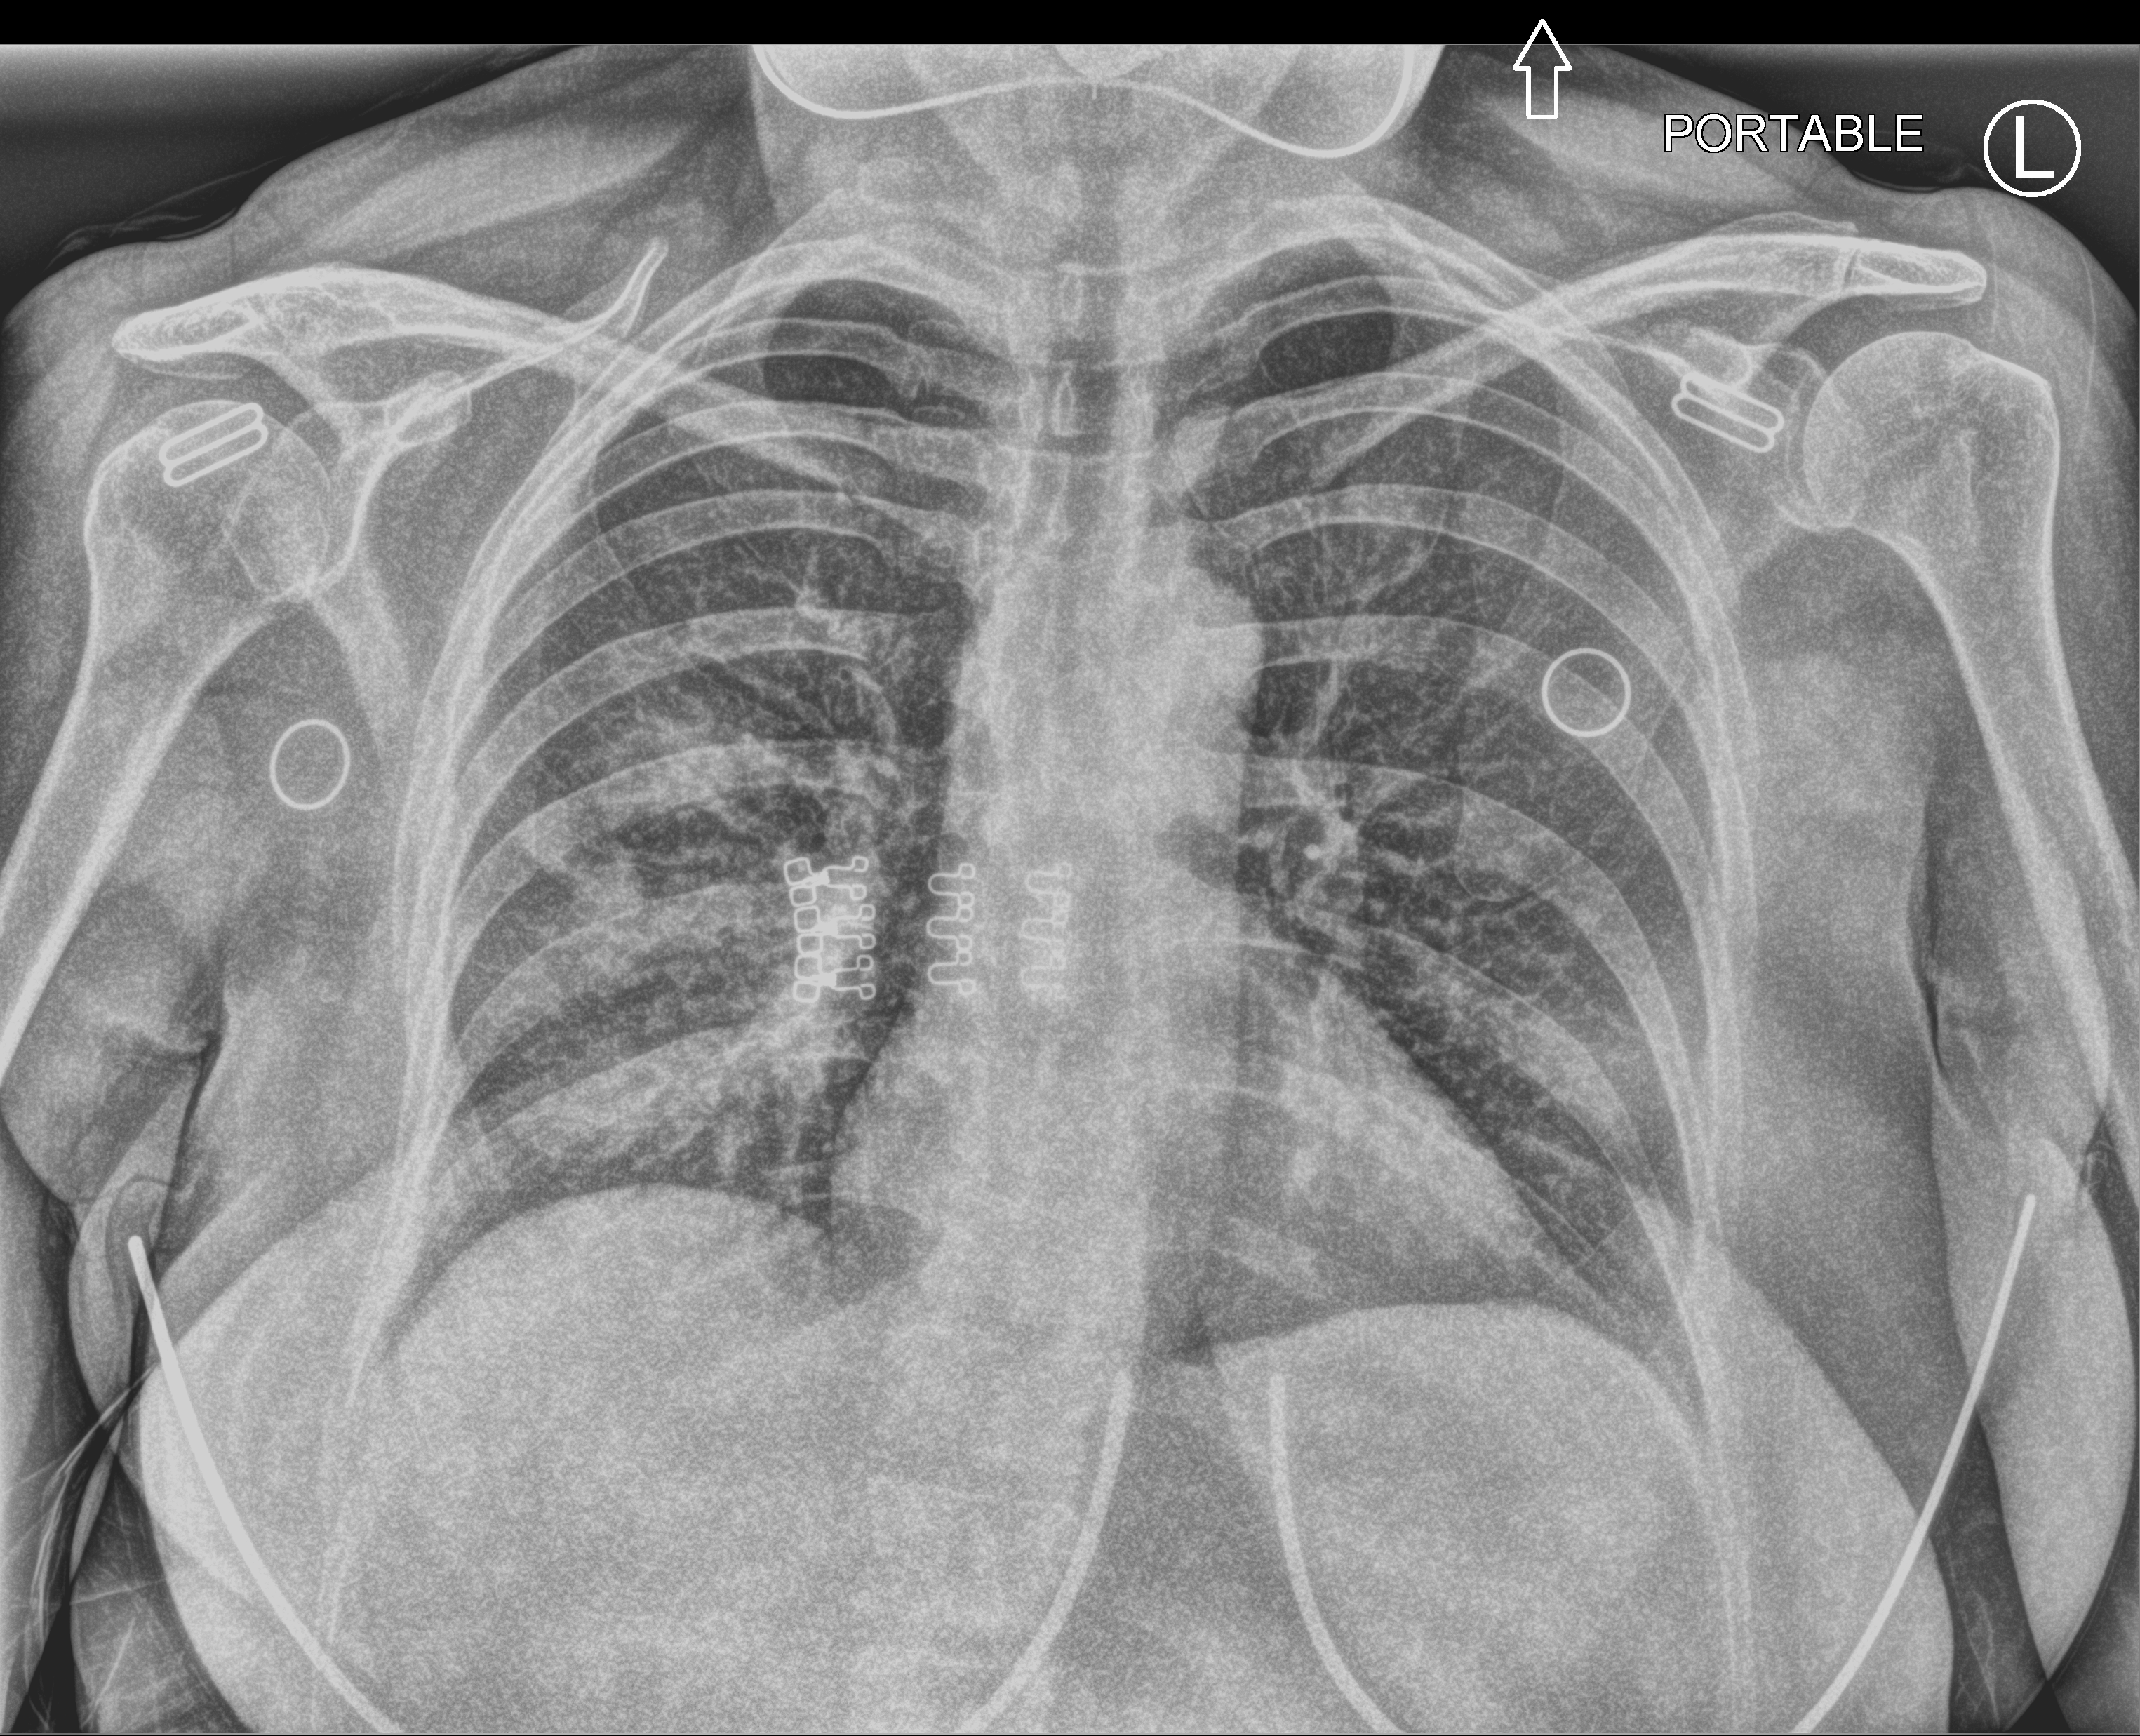
Chest X-ray (portable), anteroposterior (AP) projection. Female patient hospitalised with COVID-19, age 18–59 years.
From the hospital-stay record, not from the radiograph (when in the stay this image was taken is not recorded):
- admitted to intensive care during this hospital stay: no